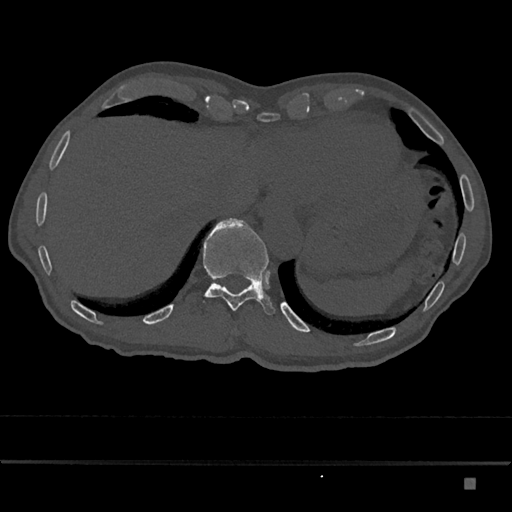
CT including the spine, one axial slice. Slice 680 of 797 in the series (ordered by position). 120 kVp. Bone window (W 1800 / L 400 HU). 512 × 512 image matrix, field of view 390 × 390 mm. Male patient, age 72 years. Case-level facts recorded for this patient, not image findings: primary cancer: prostate.
Annotated regions visible in this slice (semi-automatic segmentation, software-assisted and operator-edited):
- T11 vertebra: bounding box <203,218,275,315> (left, top, right, bottom; pixels)